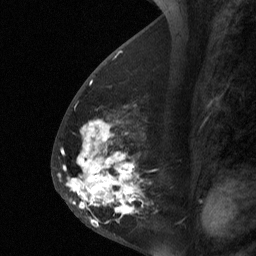
Breast MRI (dynamic contrast-enhanced), one sagittal slice. Slice 27 of 64 in the series (ordered by position). Dynamic contrast-enhanced study with each time point stored as its own series, time point 2 of 3 at this slice position (early post-contrast, ordered by acquisition time). 1.5 T. TE 4.8 ms, TR 27 ms. 256 × 256 image matrix, field of view 180 × 180 mm. Female patient, age 56 years. From the clinical record (not read from this slice): setting: breast cancer imaged before/during neoadjuvant chemotherapy; receptor status: HER2-positive.
Outlined on this slice (semi-automatically segmented with operator editing):
- analysis volume of interest (the breast-tissue region the enhancement analysis was run in; not a lesion): bounding box <59,104,149,229> (left, top, right, bottom; pixels)
- tumour enhancement mask (voxels above the 90 % enhancement threshold inside the analysis volume of interest): <59,147,138,226>